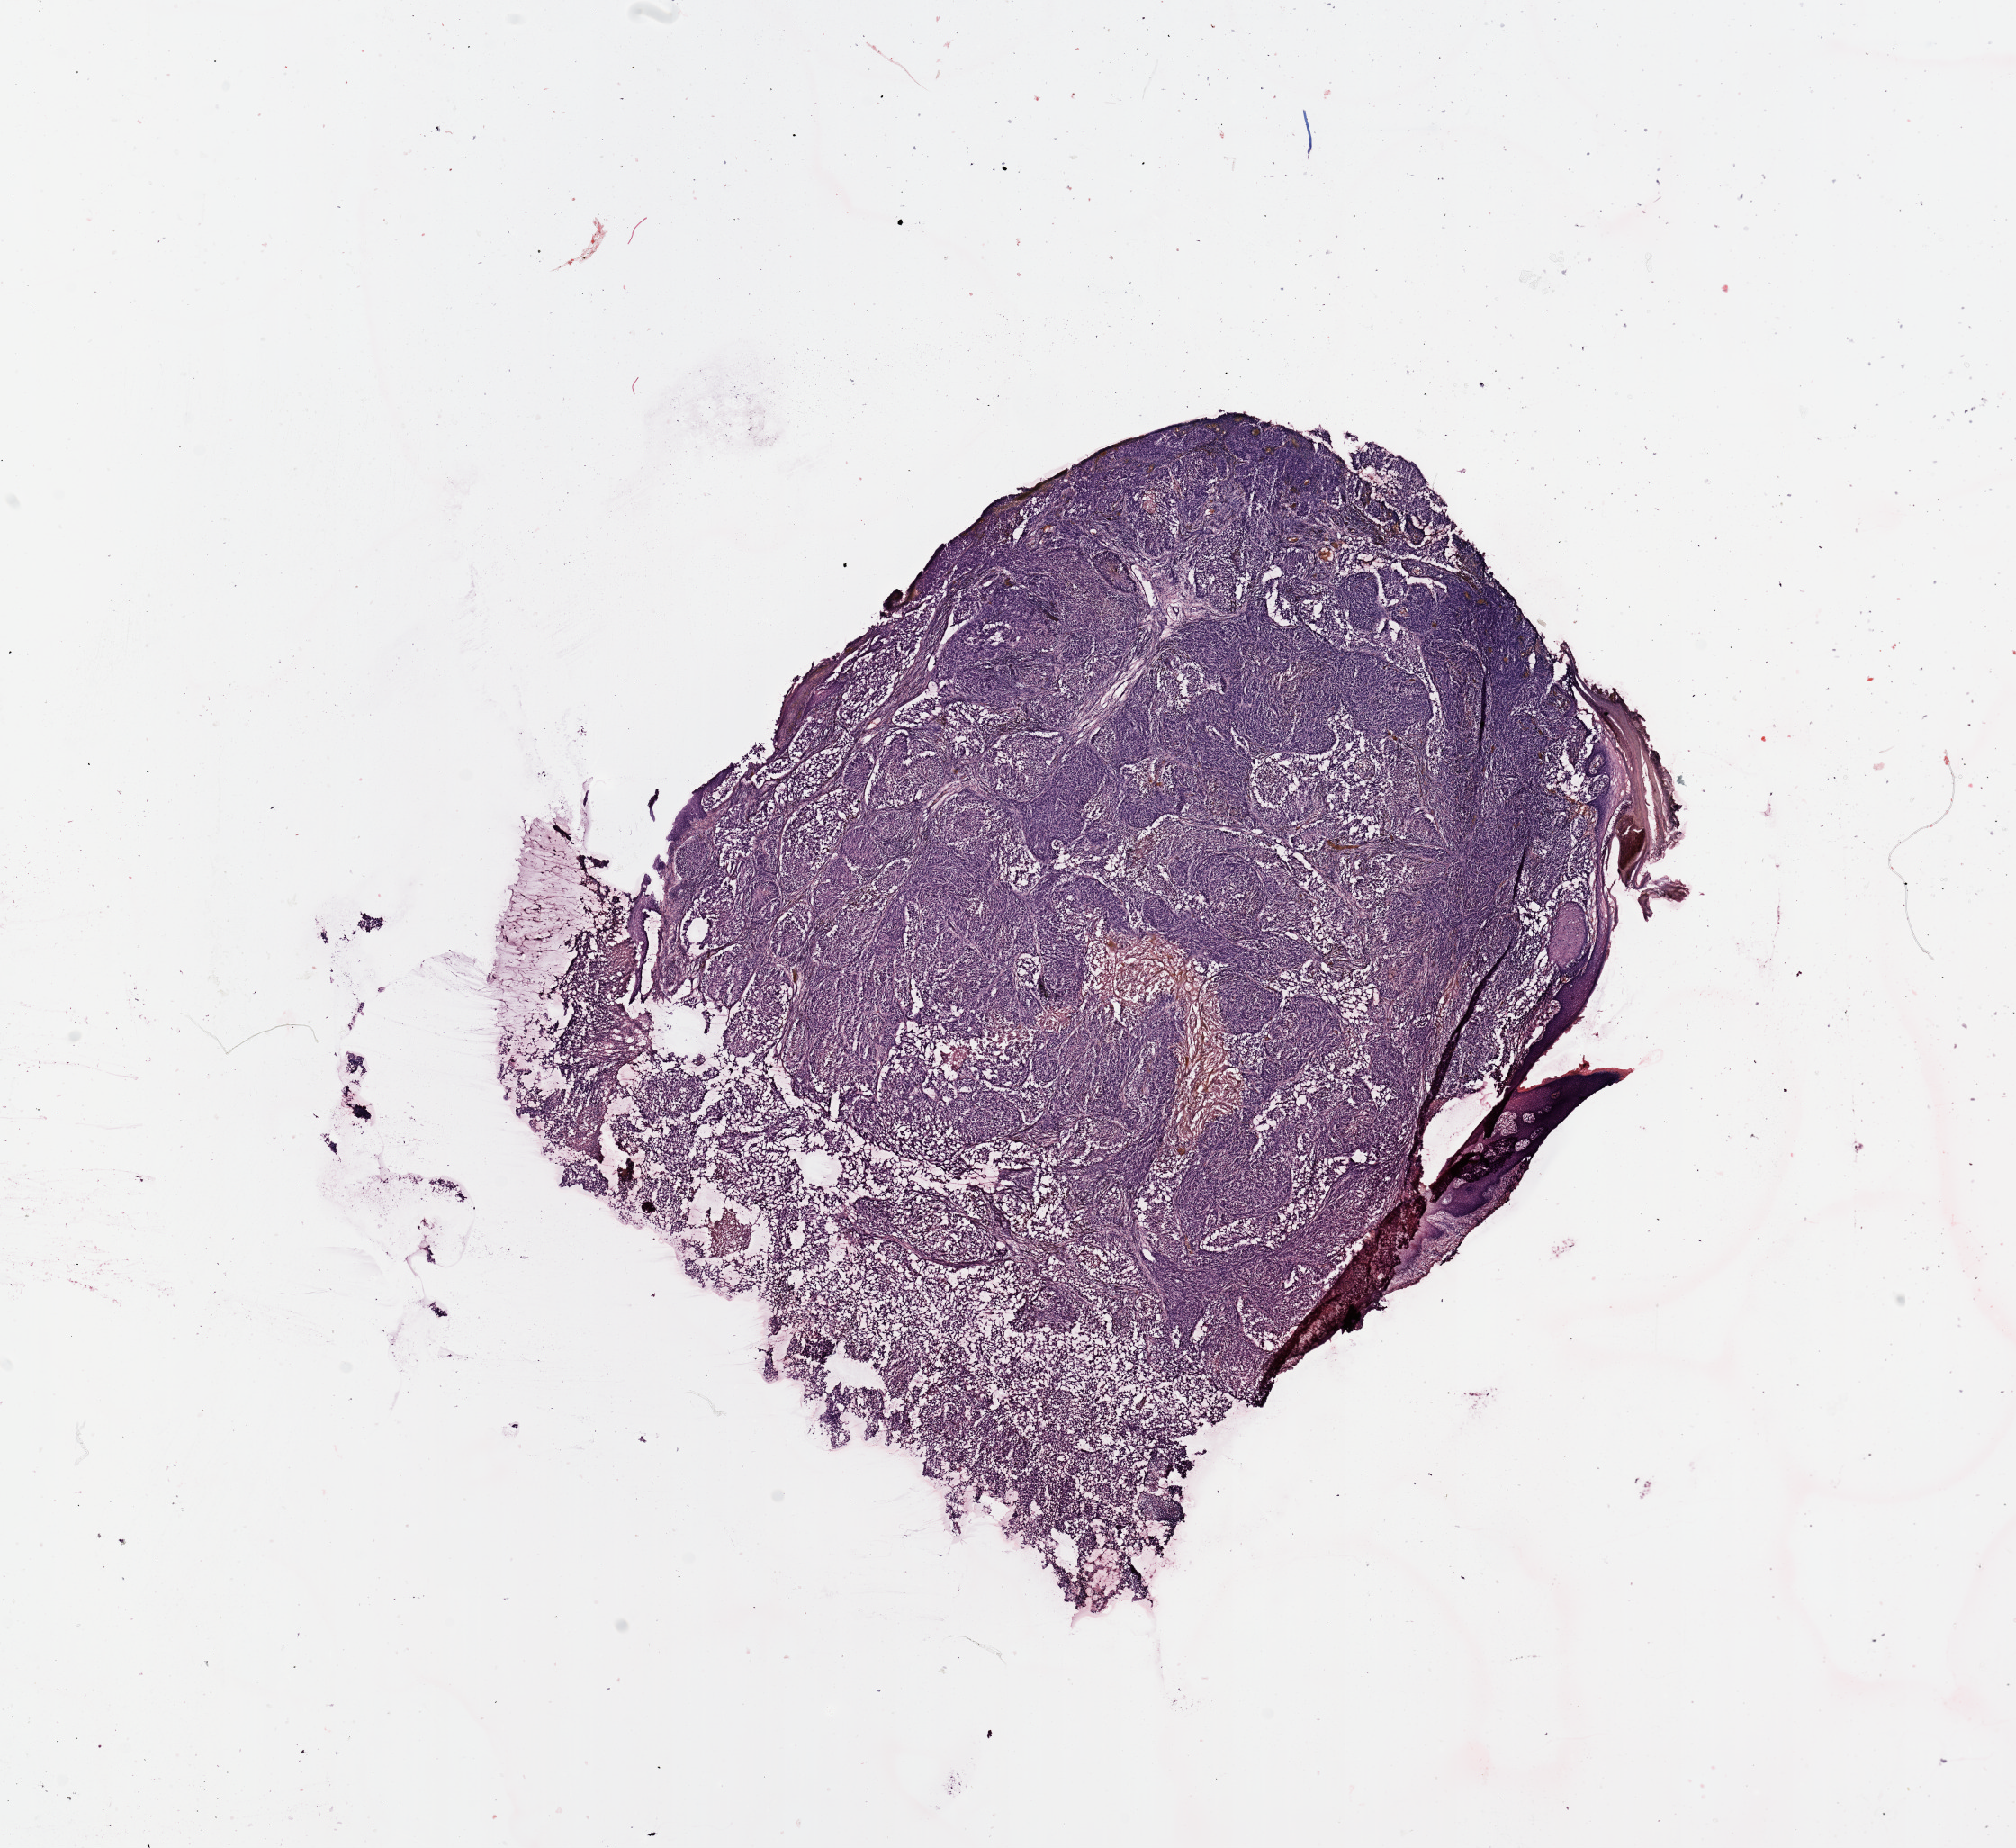
Digitized H&E-stained tissue section (whole slide), low-resolution overview of the scanned area, about 17.7 x 16.2 mm (acquisition: 20x scan); melanoma tumour tissue; sampled site not recorded. Patient: male, age 61 years.
• primary tumour site (as recorded): trunk
• patient diagnosis (cohort enrolment): cutaneous melanoma (skin)